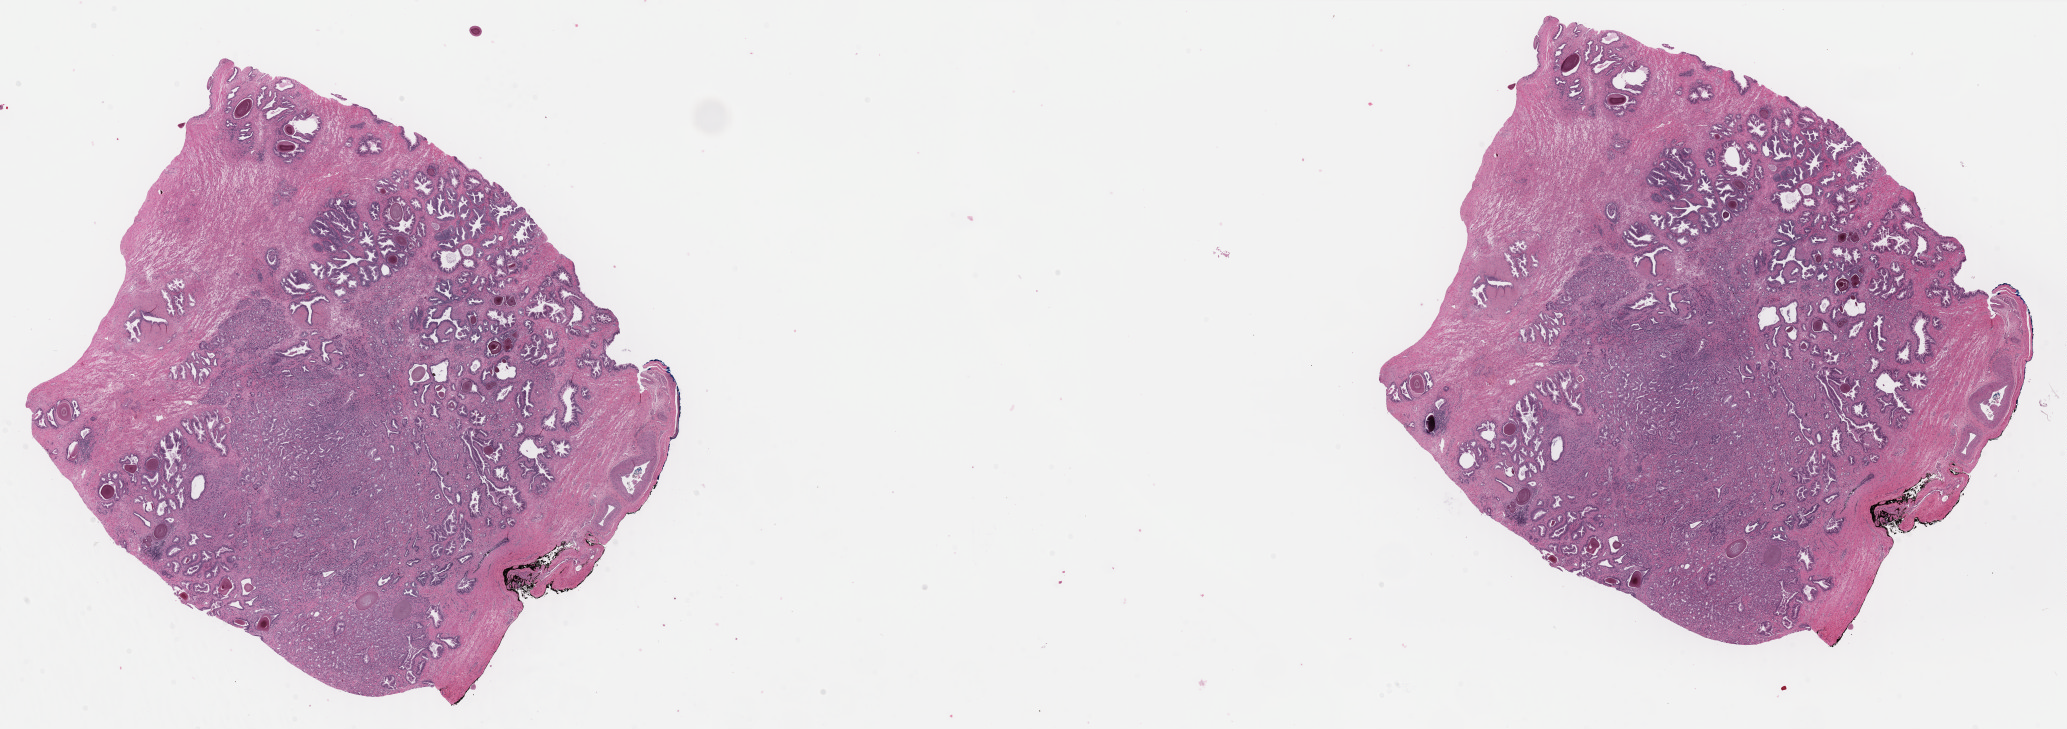
H&E whole-slide image — low-resolution overview of the scanned area, about 32.7 x 11.5 mm, formalin-fixed paraffin-embedded (FFPE) diagnostic section, prostate, primary tumour sample. Patient: male, age at initial diagnosis 70 years.
Histologic diagnosis: Adenocarcinoma, NOS (prostate gland).